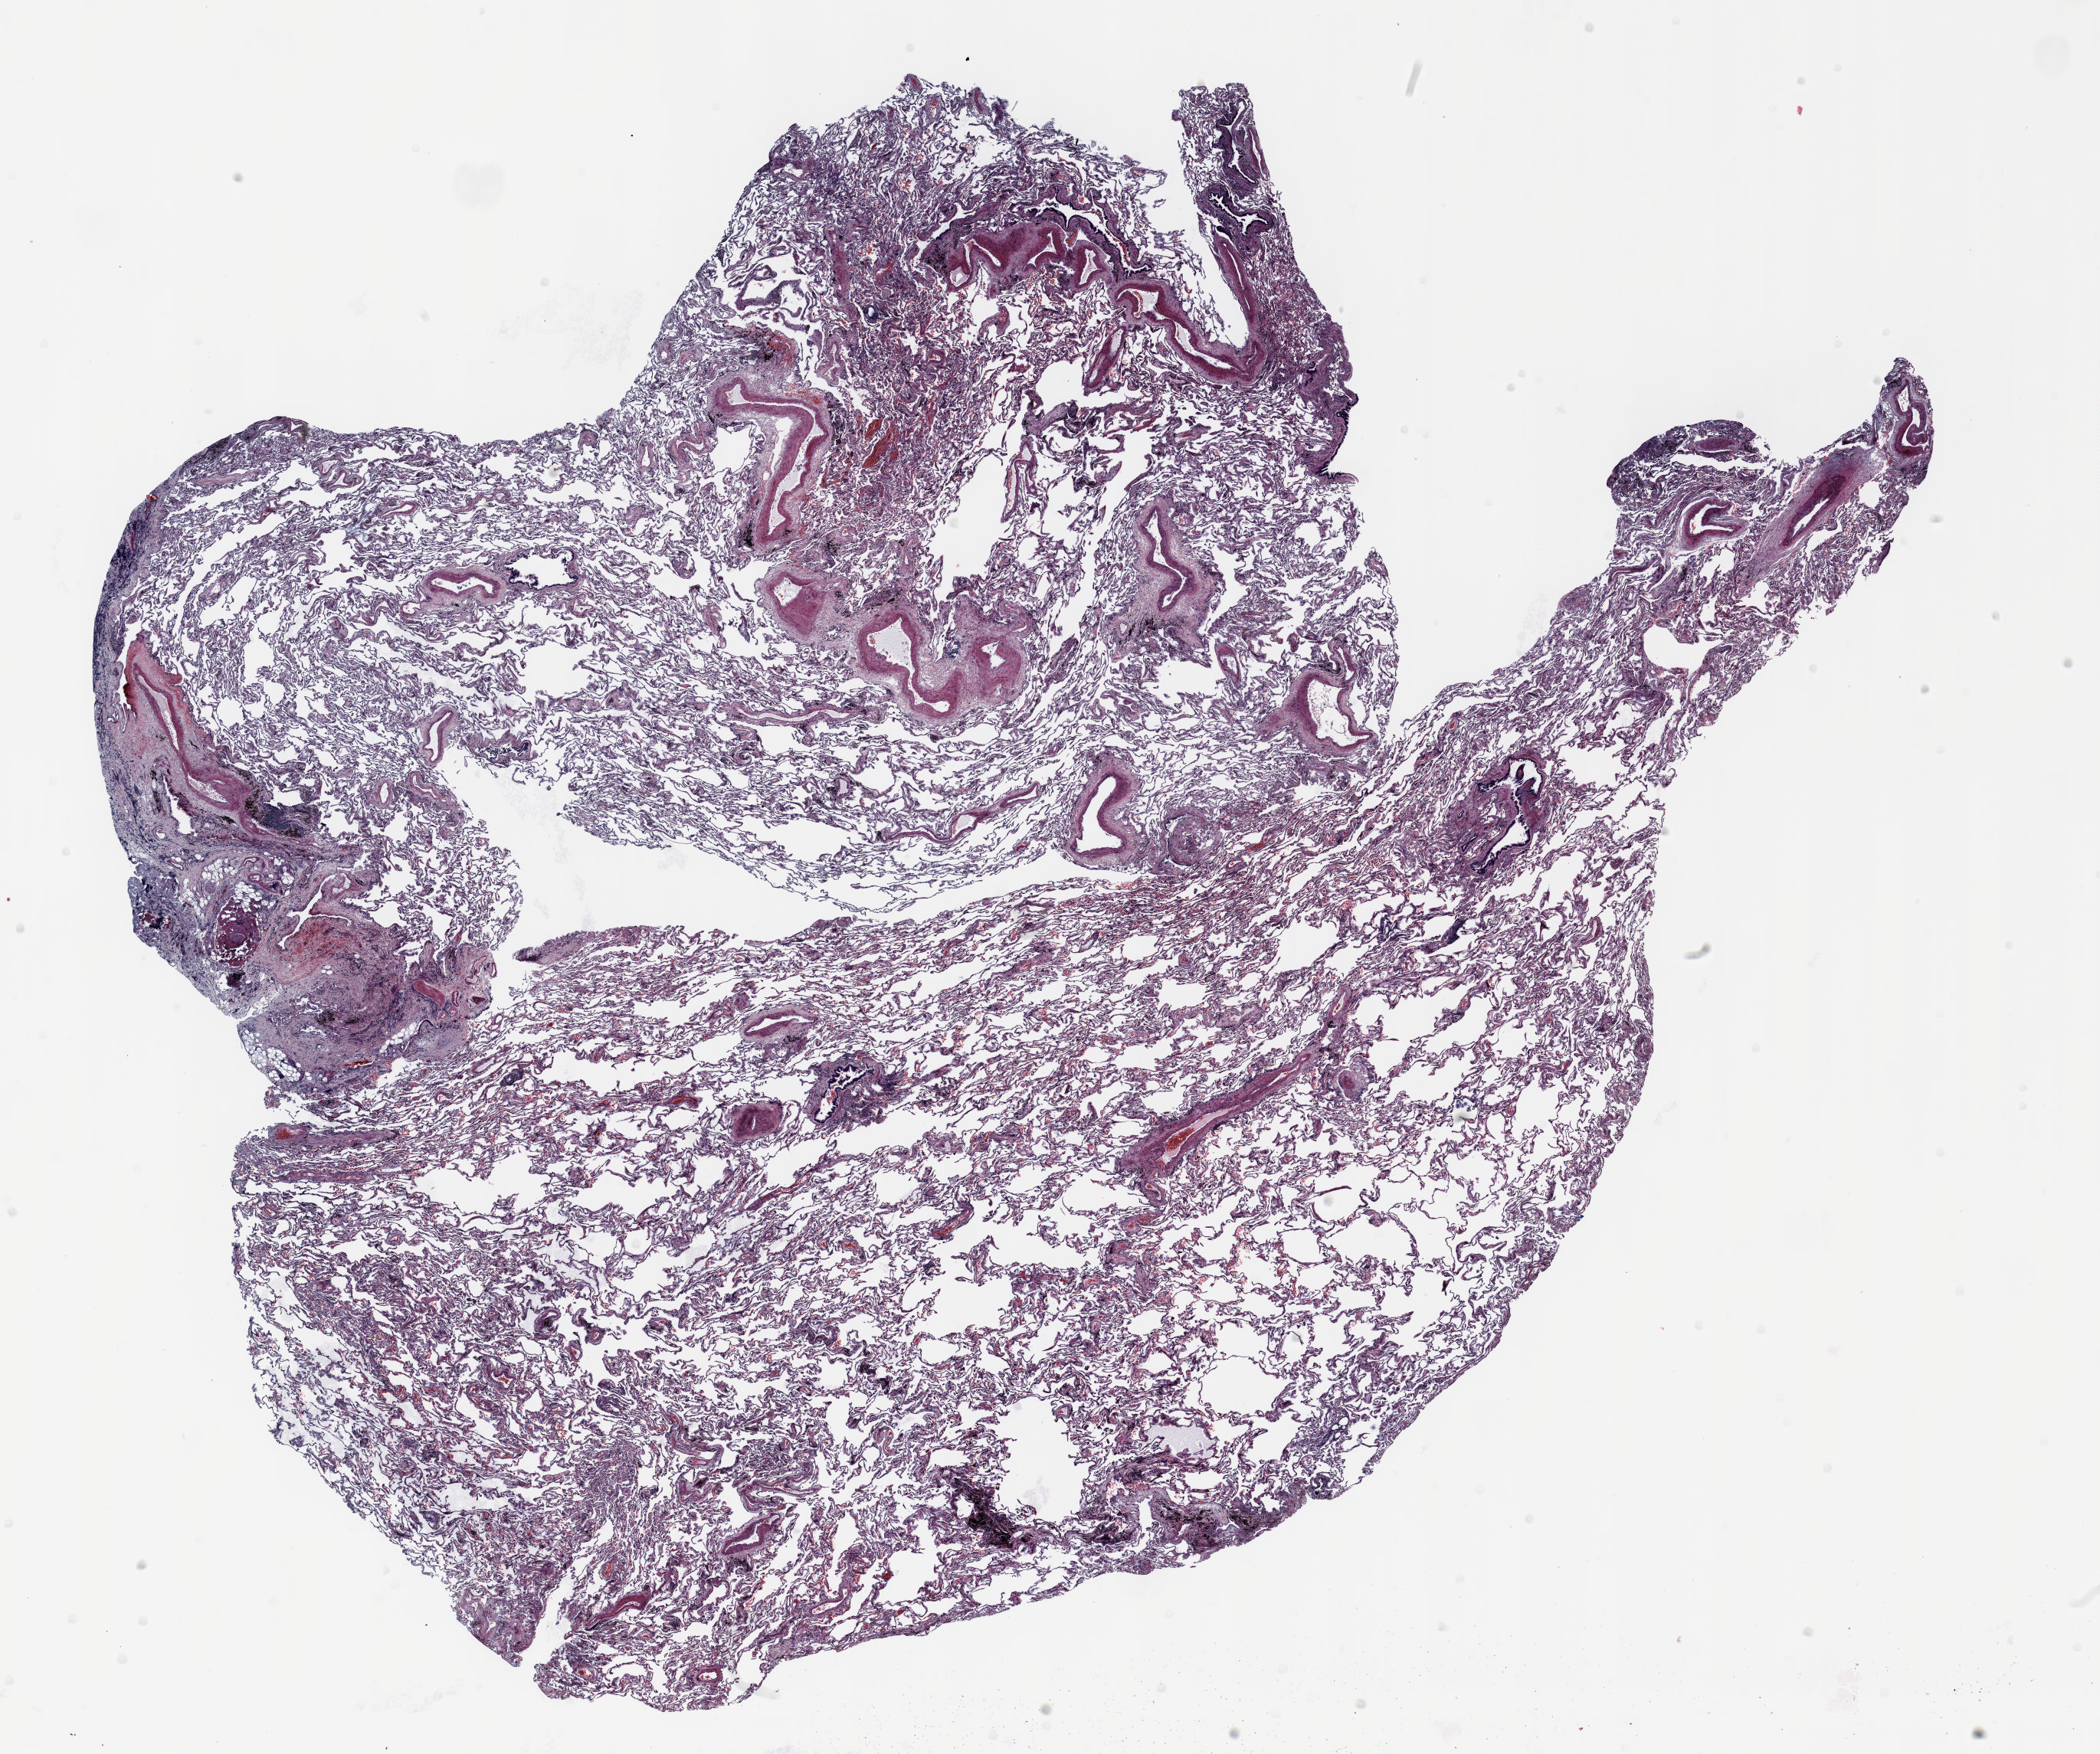
H&E whole-slide image — shown as a low-resolution overview of the whole scanned area (about 22.0 x 18.4 mm, acquisition: 20x scan), FFPE section, lung. Male patient, aged 69 at enrolment. Former smoker at enrolment. Grade: moderately differentiated (G2).
Participant's lung-cancer diagnosis: Mucinous adenocarcinoma. Primary tumour location (clinical record): right upper lobe. Stage (AJCC 6th edition): IA. ICD-O-3 topography: upper lobe of lung (C34.1). Tumour size (pathology): 11 mm.